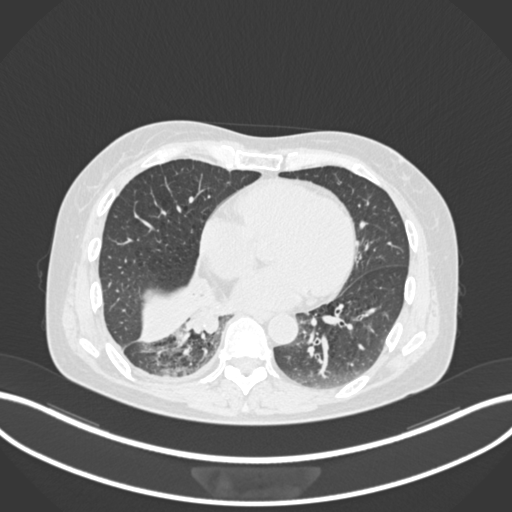
Chest CT, one axial slice; slice 59 of 168 in the series (ordered by position); reconstruction kernel B30f; 120 kVp; lung window (W 1500 / L -600 HU); 512 × 512 image matrix, field of view 400 × 400 mm. Patient: female, 63 years. From the clinical record (not read from this slice): clinical TNM (as recorded): T1c N0 M0.
Annotated regions visible in this slice (bounding box drawn by a radiologist):
- lung tumour (recorded histology: adenocarcinoma): bounding box (x1, y1, x2, y2) in pixels: (187, 300, 223, 340)